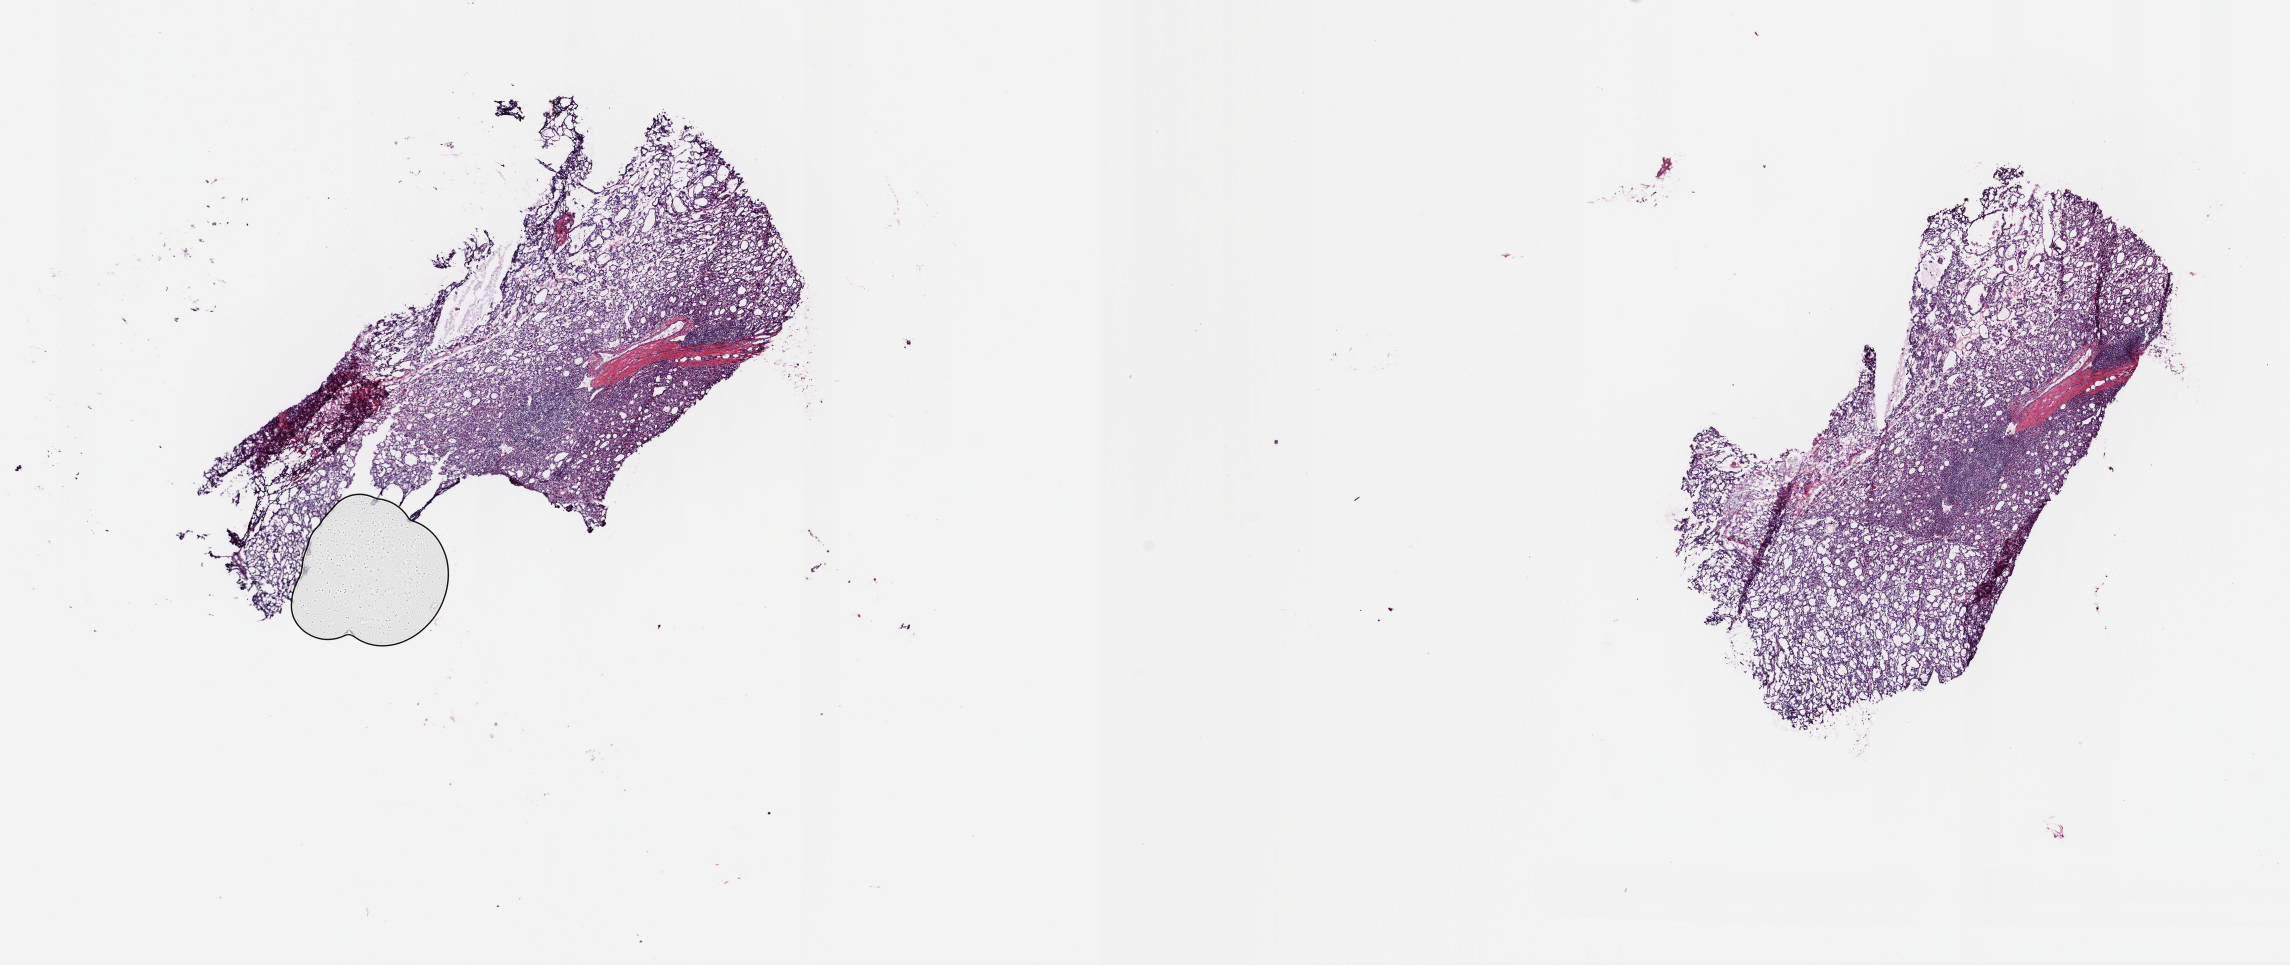
H&E-stained whole-slide image — a low-resolution overview of the entire scanned area, about 18.1 x 7.6 mm; frozen section from the top of the tissue portion; sample: primary tumour, thyroid. Patient: male, age at initial diagnosis 39 years. Slide review estimates, as recorded: tumour cells 90%, tumour nuclei 85%, normal cells 0%, stromal cells 10%, necrosis 0%. Inflammatory infiltration, as recorded: lymphocyte infiltration 10%, monocyte infiltration 2%, neutrophil infiltration 0%.
Diagnosis: Papillary carcinoma, follicular variant. AJCC pathologic stage: I (7th edition). TNM: T3 N1a MX. Laterality: right. Lymph nodes positive (case pathology): 4 of 24 examined.